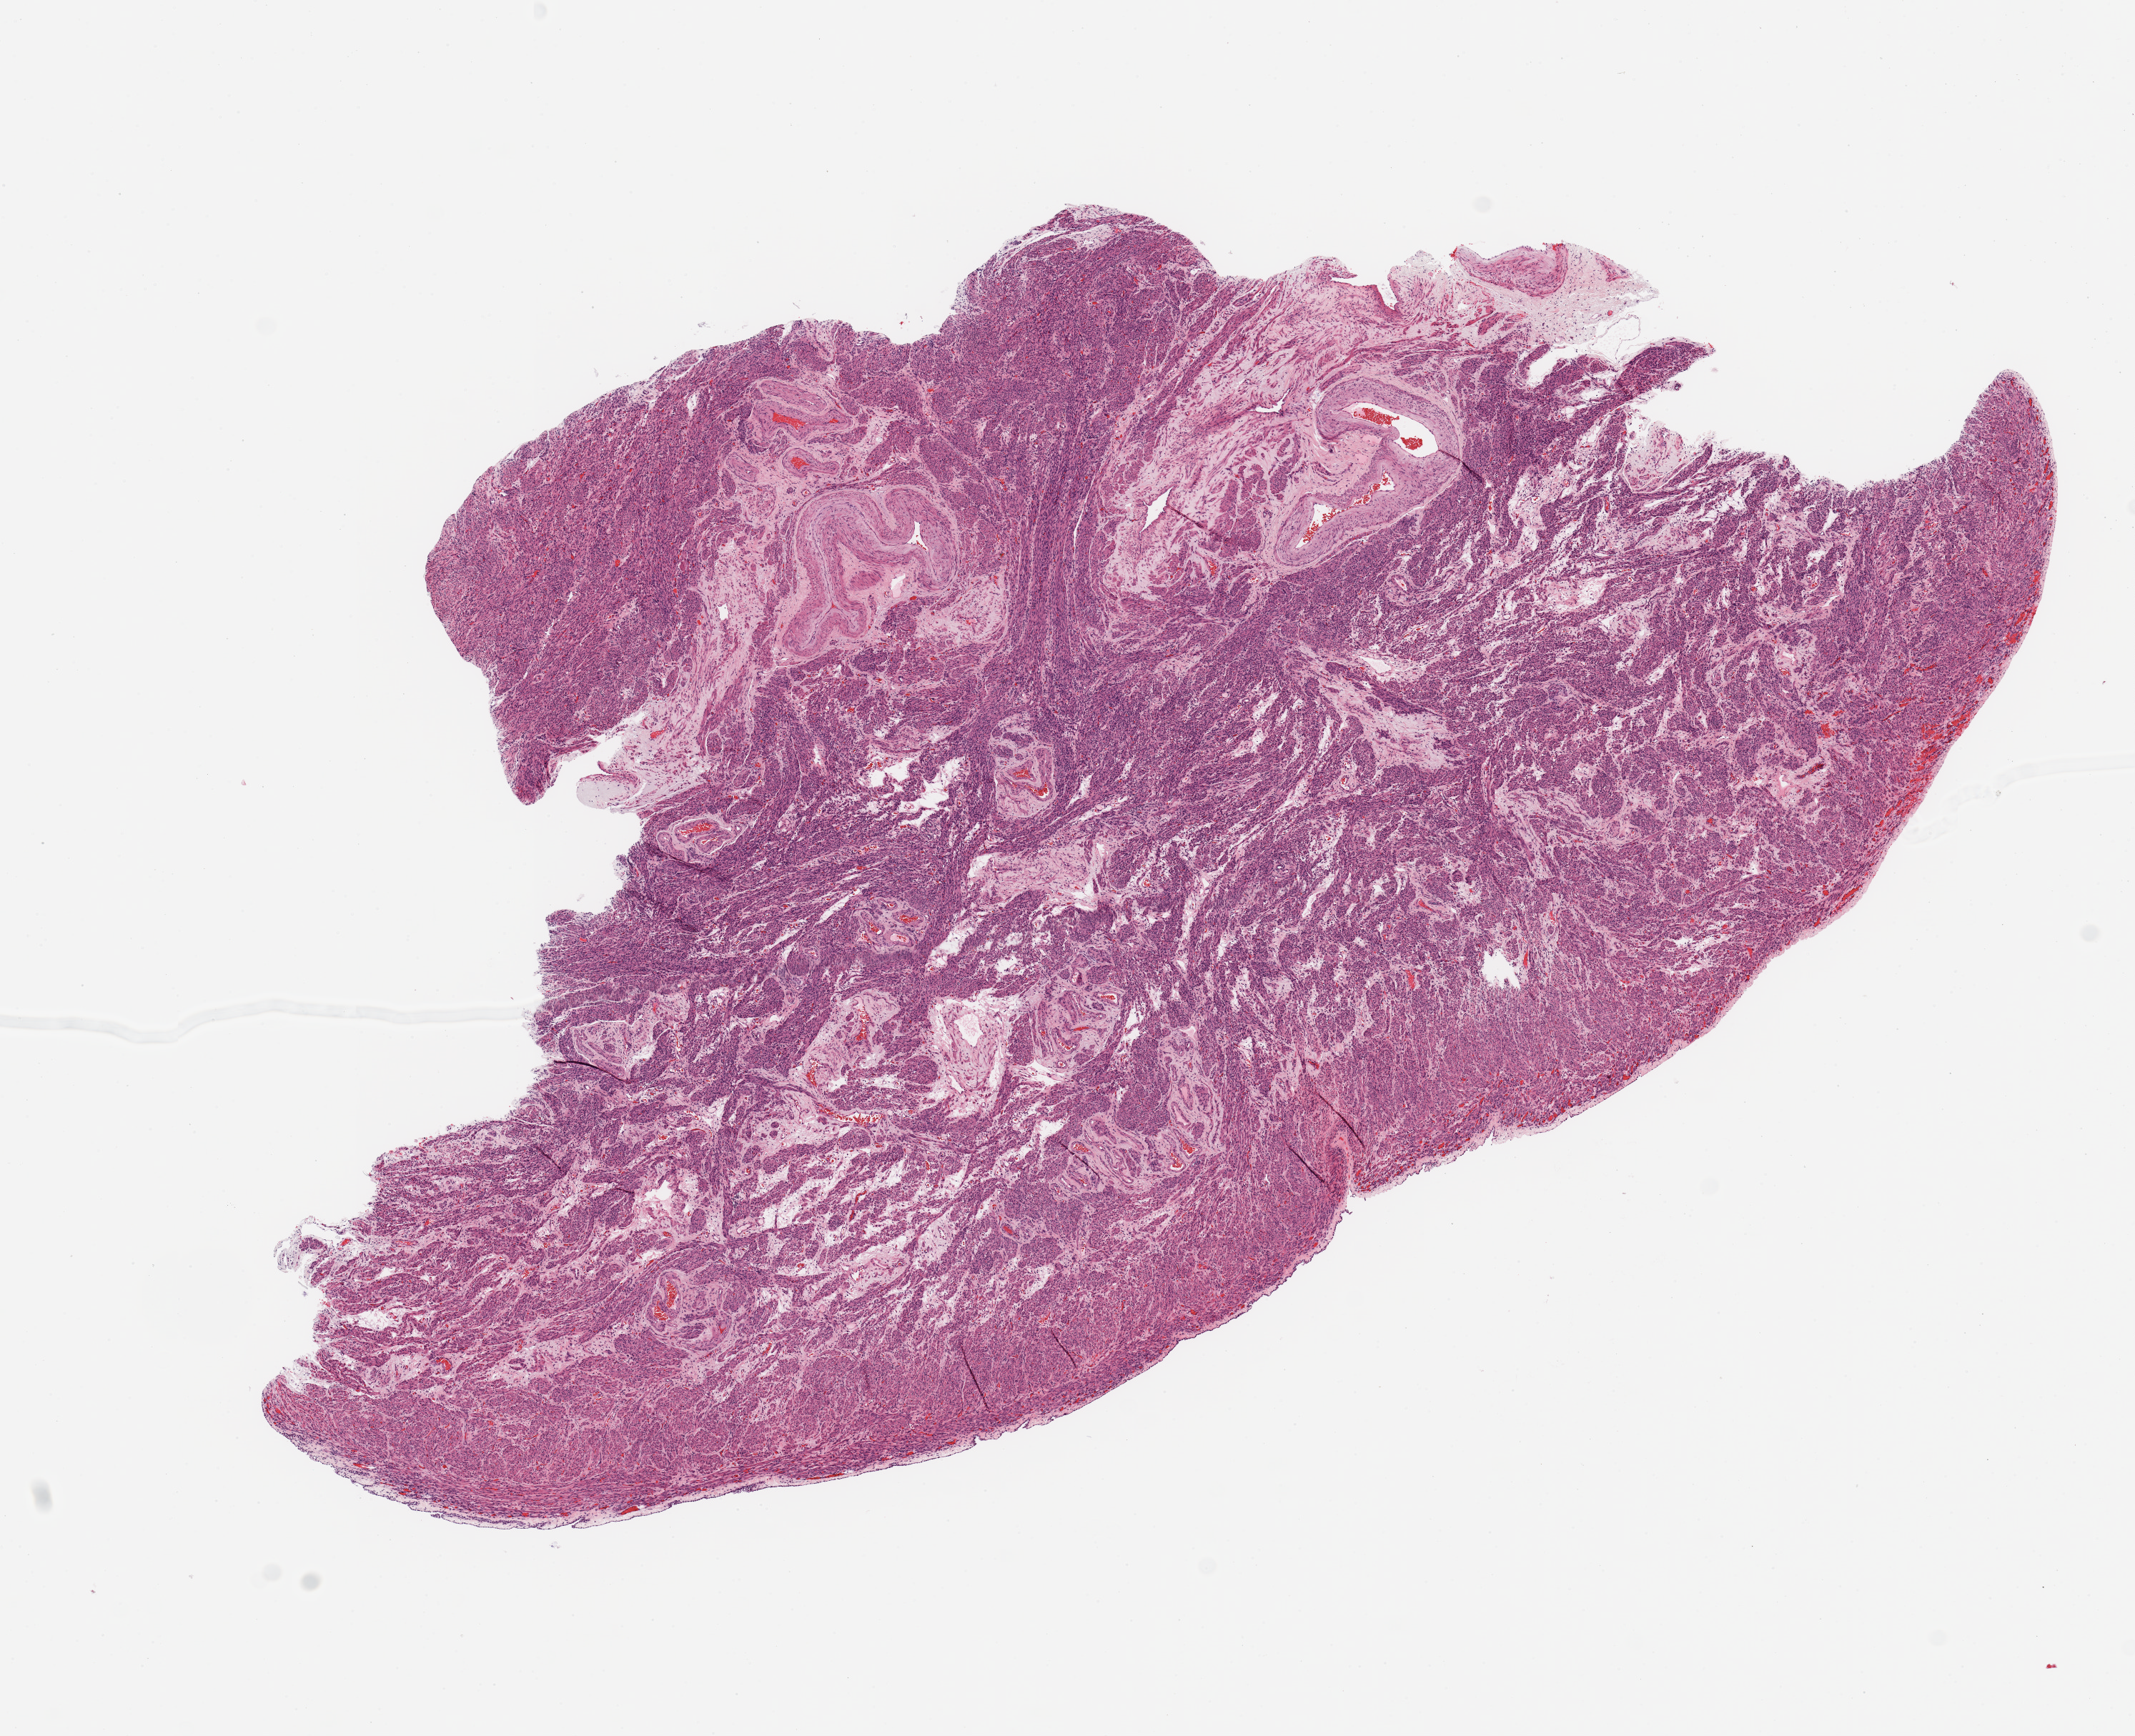
H&E whole-slide image, whole scanned area (about 11.8 x 9.6 mm, slide scanned at 20x) shown as a low-resolution overview; normal (non-tumour) tissue sample, uterus. Patient: female, aged 90 or older.
This section: normal (non-tumour) tissue from the same patient. Patient diagnosis: Endometrioid adenocarcinoma, NOS.